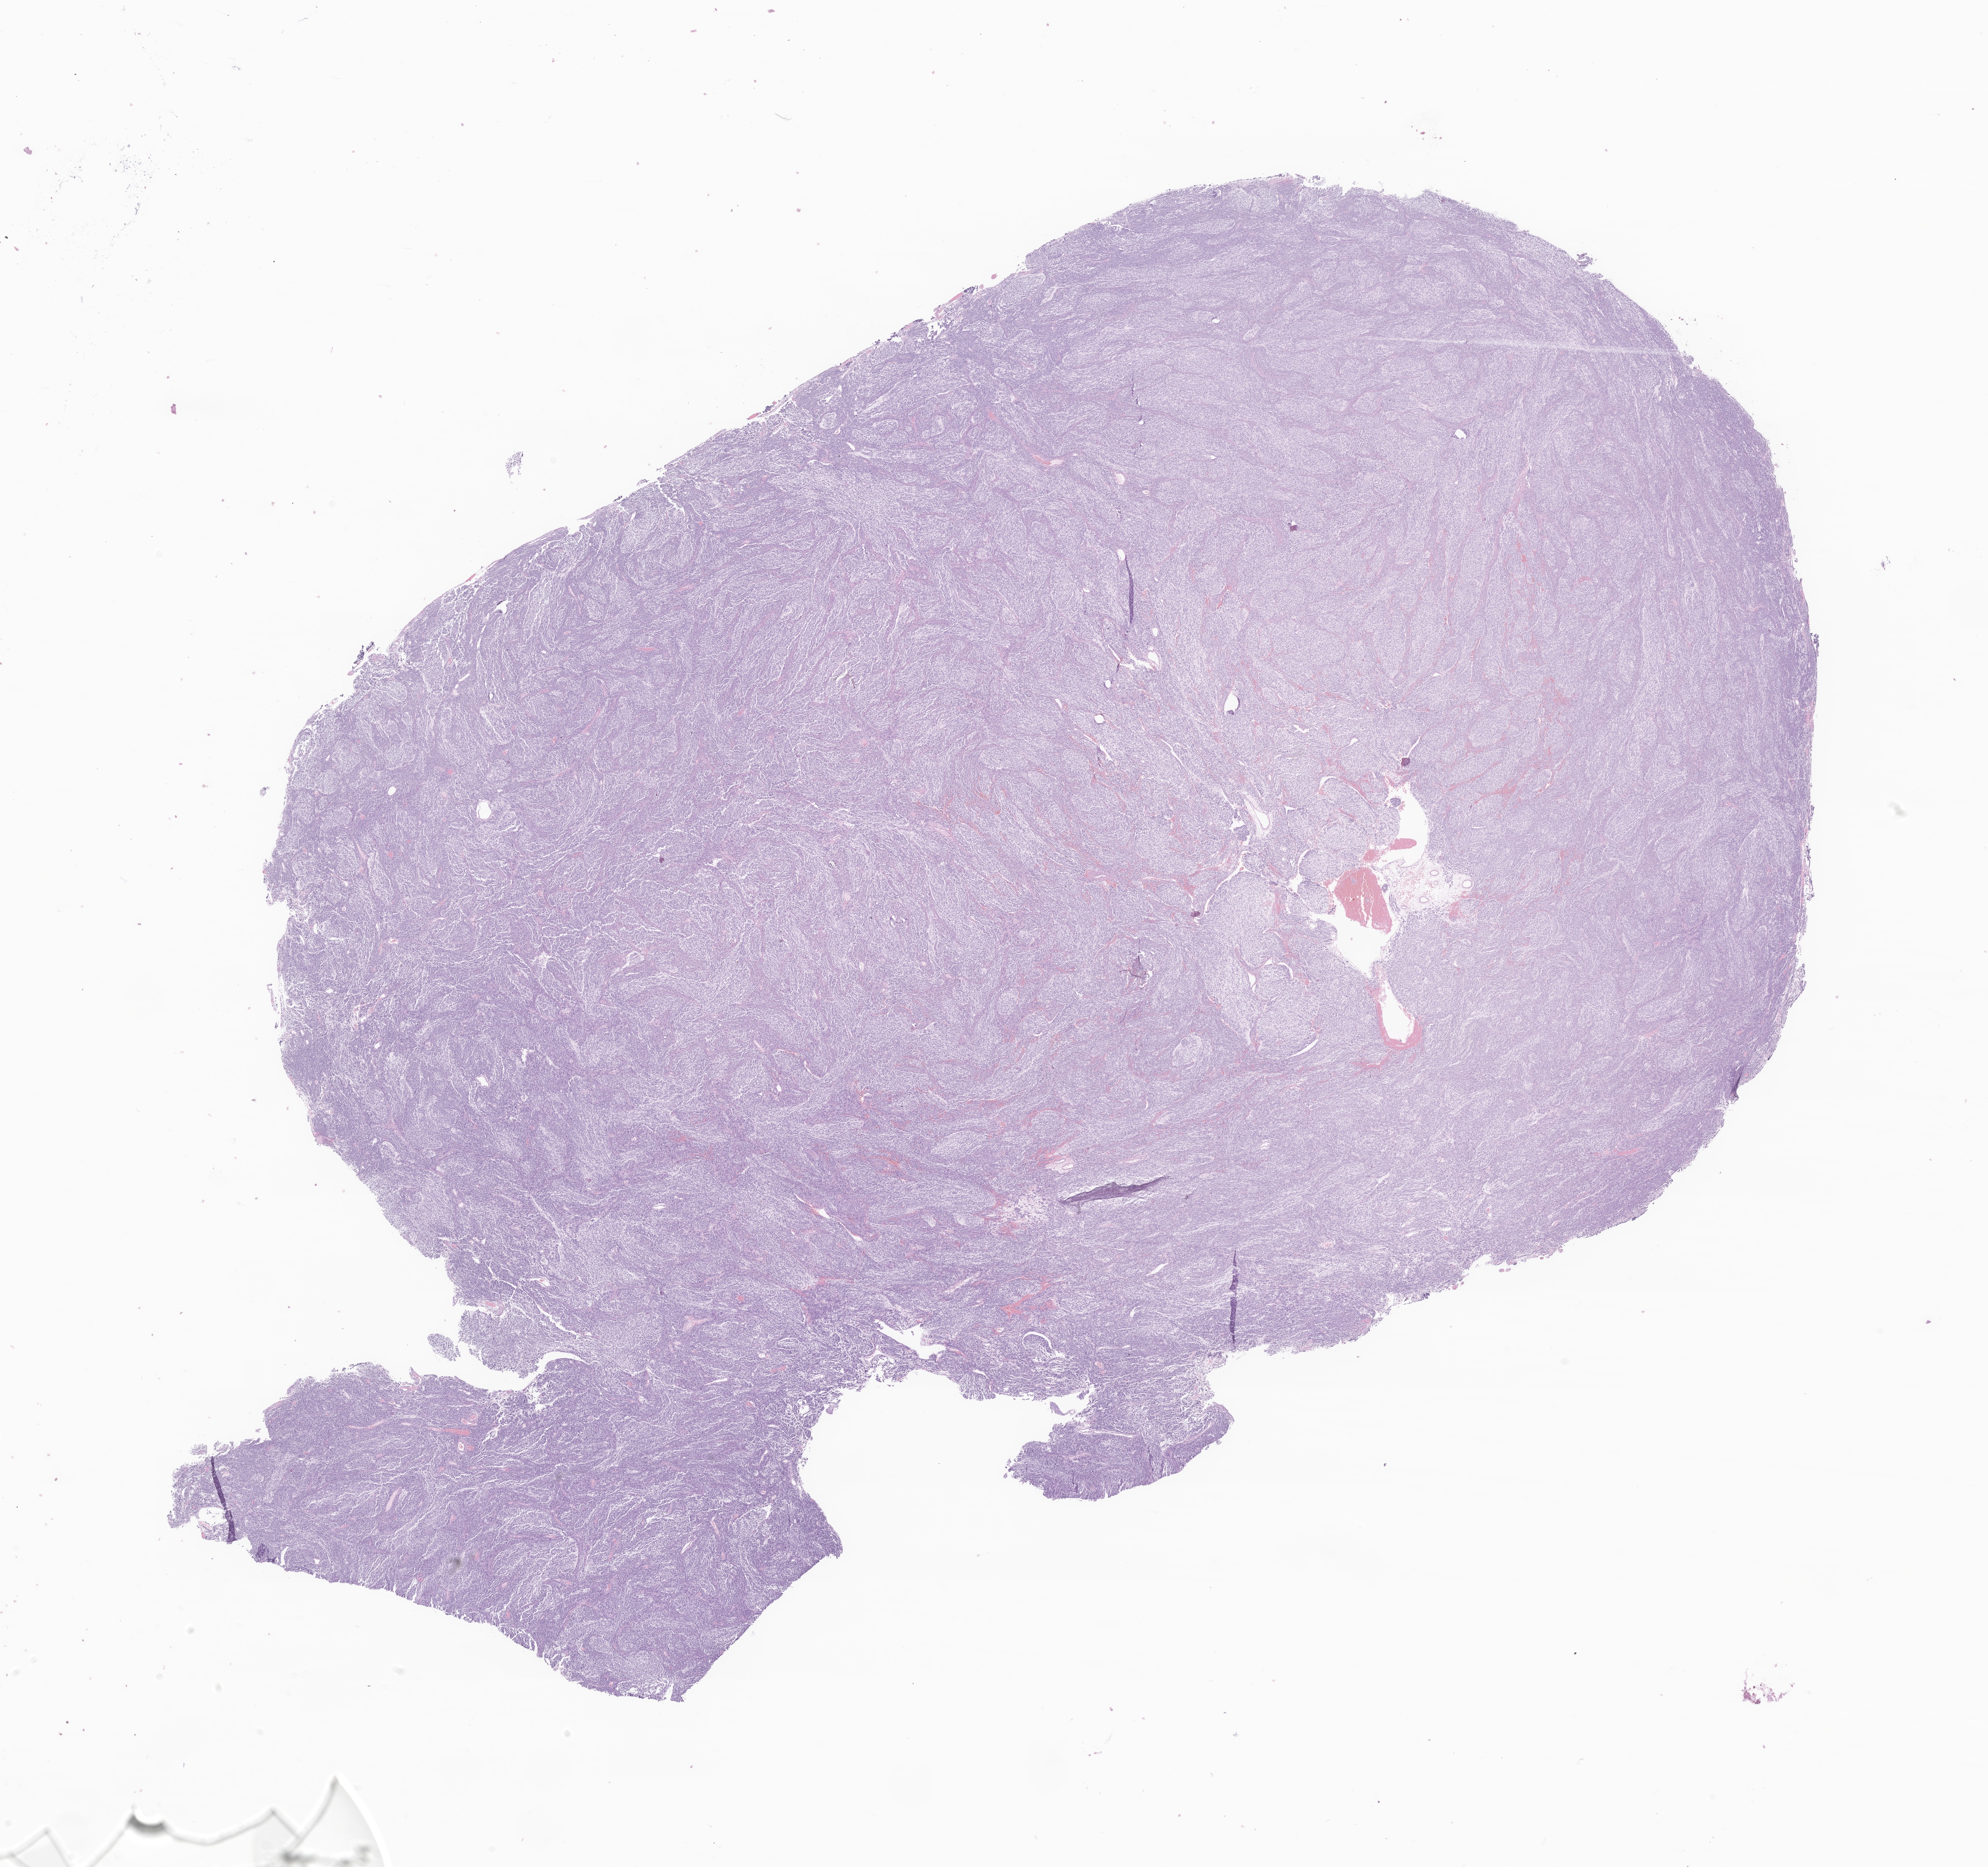
Whole-slide image, hematoxylin and eosin (H&E) stain of tumor tissue from the brain stem — a low-resolution overview of the entire scanned area, about 21.9 x 20.6 mm, FFPE section. Patient: male, age 786 days (about 2.2 years).
Diagnosis: Medulloblastoma, NOS.